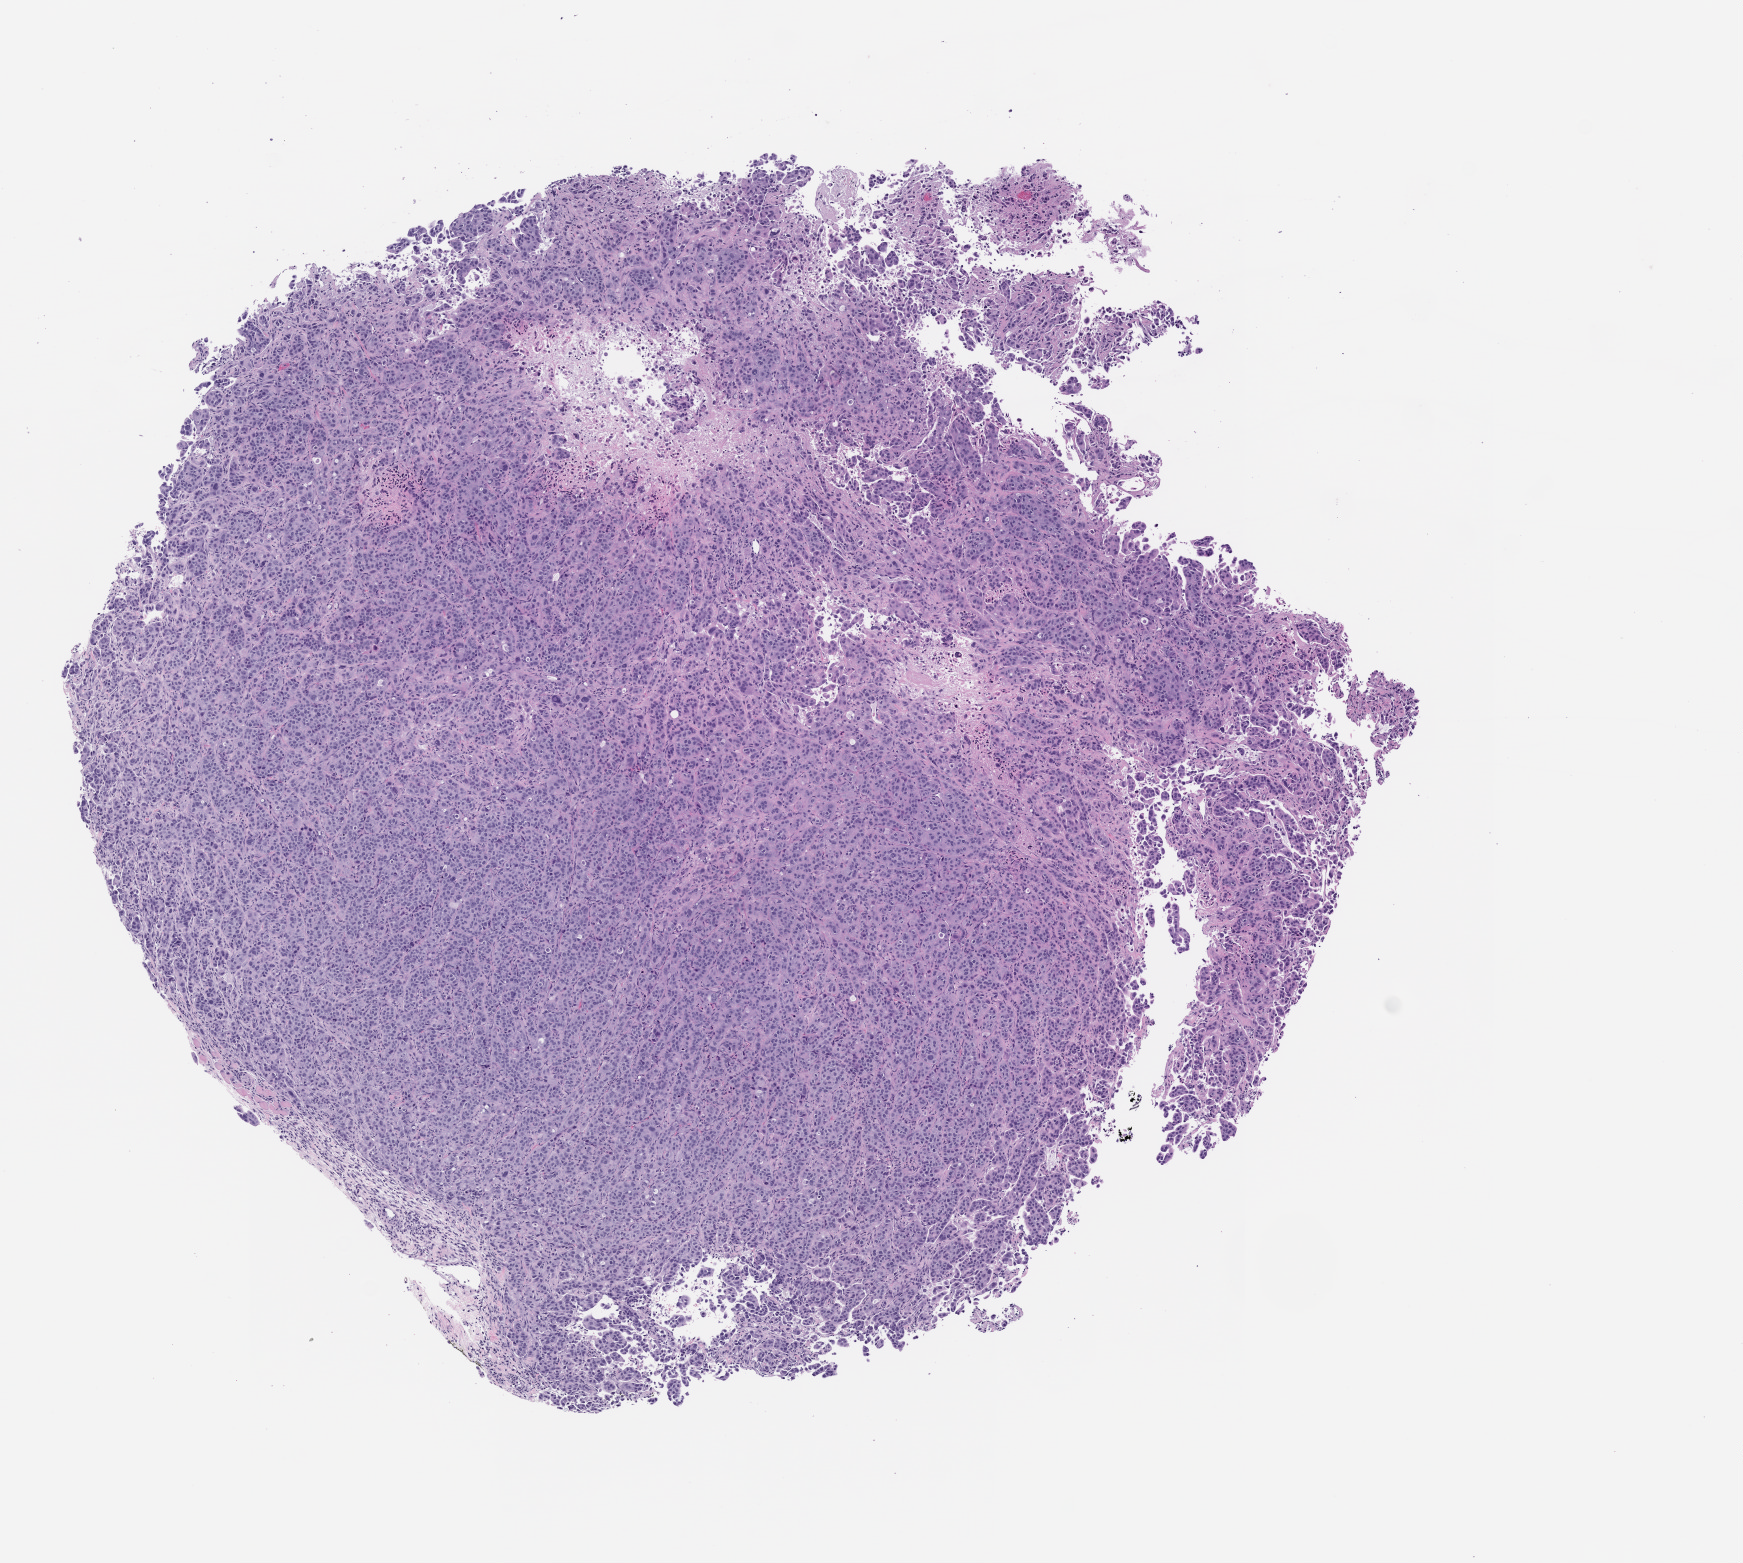
Hematoxylin and eosin (H&E) whole-slide image of a patient-derived xenograft (PDX) tumor grown in a mouse — low-resolution overview of the scanned area, about 7.0 x 6.3 mm. Formalin-fixed paraffin-embedded section. Originating tumor site category: lung.
Originating patient diagnosis: Lung Squamous Cell Carcinoma.